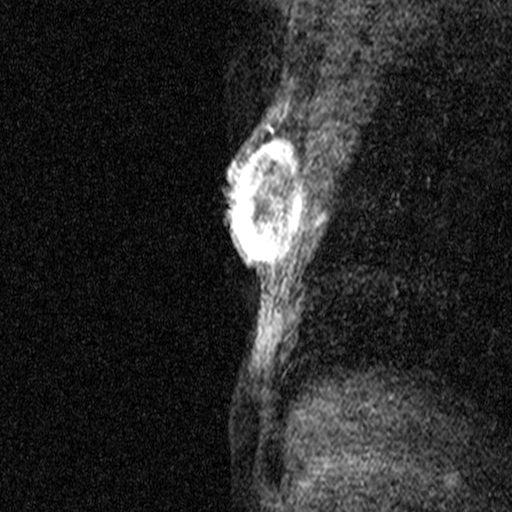
Breast MRI (dynamic contrast-enhanced), one sagittal slice; position 29 of 44 along the scan axis; dynamic contrast-enhanced study with each time point stored as its own series, time point 2 of 3 at this slice position (early post-contrast, ordered by acquisition time); 1.5 T; TE 4.5 ms, TR 11 ms; 3 mm slice thickness; 512 × 512 image matrix, field of view 200 × 200 mm. Female patient, age 44 years. From the clinical record (not read from this slice): setting: breast cancer imaged before/during neoadjuvant chemotherapy; receptor status: HR-positive, HER2-negative.
Structures marked on this image (semi-automatically segmented with operator editing):
- analysis volume of interest (the breast-tissue region the enhancement analysis was run in; not a lesion): bounding box <218,118,304,291> (left, top, right, bottom; pixels)
- tumour enhancement mask (voxels above the 90 % enhancement threshold inside the analysis volume of interest): <228,125,304,259>